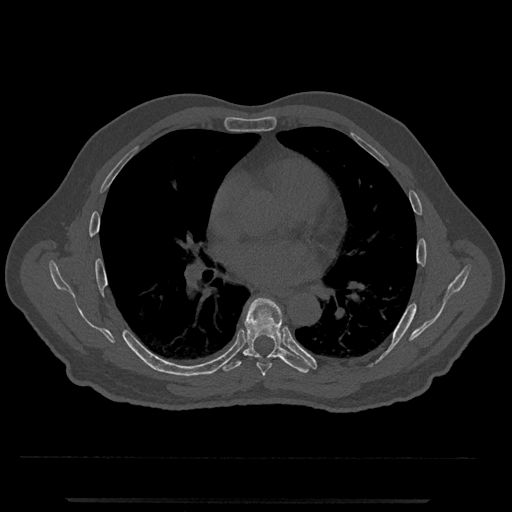
CT including the spine, one axial slice; position 707 of 797 along the scan axis; reconstruction kernel Br40s/3; 120 kVp; bone window (W 1800 / L 400 HU); 0.5 mm slice thickness; 512 × 512 image matrix, field of view 419 × 419 mm. Patient: male, 63 years. Case-level facts recorded for this patient, not image findings: primary cancer: prostate.
Outlined on this slice (semi-automatic segmentation, software-assisted and operator-edited):
- T6 vertebra: bounding box [x1, y1, x2, y2] px = [256, 362, 272, 376]
- T7 vertebra: [220, 297, 314, 373]